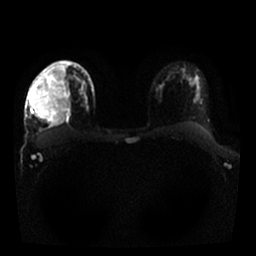
Breast MRI, one axial slice; slice 13 of 25 in the series (ordered by position); diffusion-weighted series; image 2 of 4 stored at this slice position (different b-values; order by instance number); 1.5 T; 4 mm slice thickness; 256 × 256 image matrix, field of view 330 × 330 mm. Female patient.
Outlined on this slice (expert manual segmentation):
- tumour on diffusion-weighted imaging: bounding box <65,111,71,116> (left, top, right, bottom; pixels)